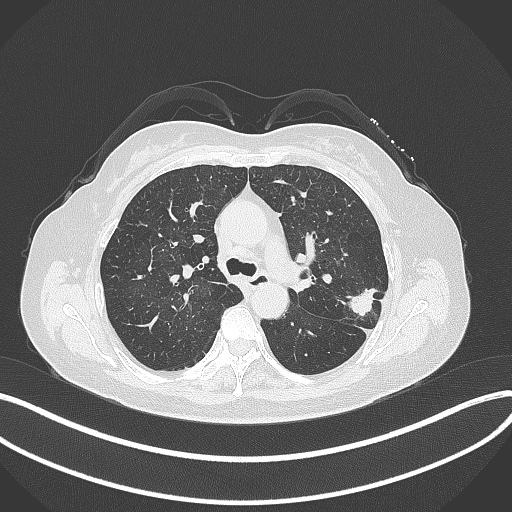
Chest CT, one axial slice; slice 214 of 319 in the series (ordered by position); reconstruction kernel B70f; lung window (W 1500 / L -600 HU); 512 × 512 image matrix, field of view 400 × 400 mm. Patient: female, 60 years. From the clinical record (not read from this slice): clinical TNM (as recorded): T1c N0 M0.
Outlined on this slice (bounding box drawn by a radiologist):
- lung tumour (recorded histology: adenocarcinoma): box from (x=345, y=280) to (x=377, y=318) px